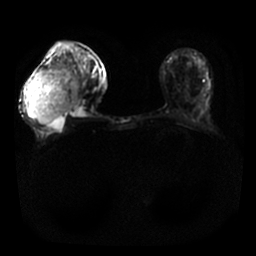
Breast MRI, one axial slice; position 3 of 25 along the scan axis; diffusion-weighted series; image 2 of 4 stored at this slice position (different b-values; order by instance number); 1.5 T; 4 mm slice thickness; 256 × 256 image matrix. Female patient.
Structures marked on this image (expert manual segmentation):
- tumour on diffusion-weighted imaging: bounding box (x1, y1, x2, y2) in pixels: (29, 68, 79, 125)